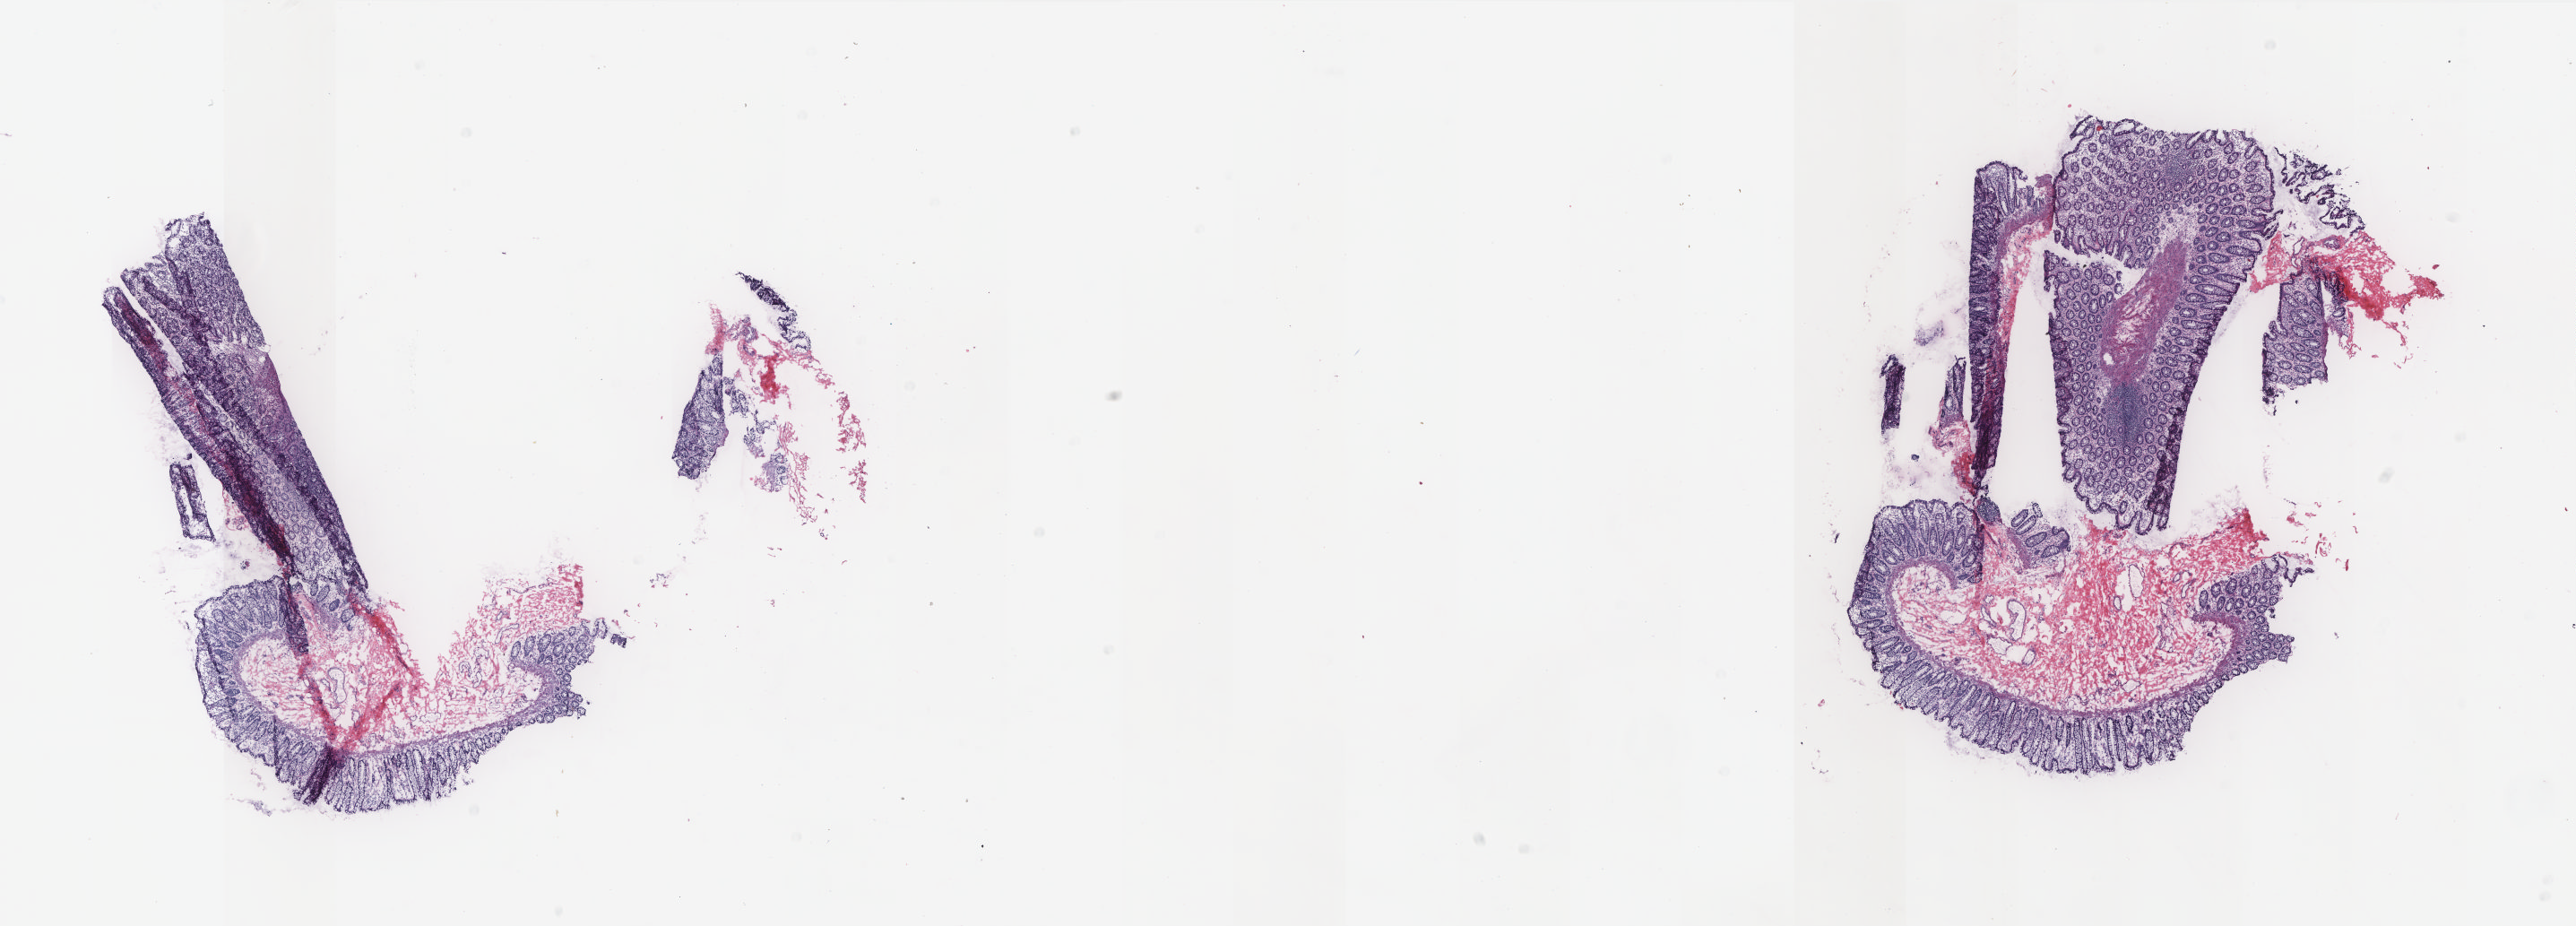
Whole-slide histology image, Hematoxylin and eosin (H&E) stained, shown as a low-resolution overview of the whole scanned area (about 23.0 x 8.3 mm, acquisition: 20x scan), frozen section from the bottom of the tissue portion, solid tissue normal (non-tumour tissue) sample from the colon. Female patient; age at initial diagnosis 63 years. Pathologist review of this section (percent, as recorded): tumour cells 0%, normal cells 100%. Inflammatory infiltration, as recorded: lymphocyte infiltration 35%, monocyte infiltration 8%, neutrophil infiltration 0%.
This section: solid tissue normal sample (biorepository sample class). Patient diagnosis: Adenocarcinoma, NOS (sigmoid colon).